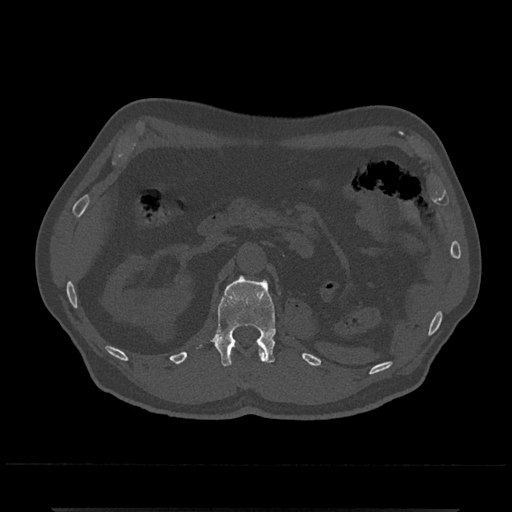
CT including the spine, one axial slice; position 376 of 797 along the scan axis; reconstruction kernel Br40s/3; 120 kVp; bone window (W 1800 / L 400 HU); 0.5 mm slice thickness; 512 × 512 image matrix. Male patient, age 67 years. Case-level facts recorded for this patient, not image findings: primary cancer: prostate.
Structures marked on this image (semi-automatically segmented with operator editing):
- L1 vertebra: box from (x=197, y=275) to (x=276, y=367) px
- T12 vertebra: (x=231, y=346)–(x=267, y=361)